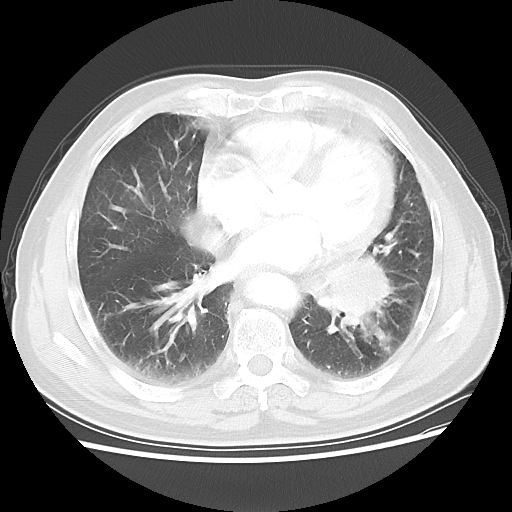
Chest CT, one axial slice; slice 25 of 56 in the series (ordered by position); reconstruction kernel LUNG; 120 kVp; lung window (W 1500 / L -600 HU); 5 mm slice thickness; 512 × 512 image matrix. Patient: male, 75 years. Case-level facts recorded for this patient, not image findings: clinical TNM (as recorded): T3 N0 M0.
Annotated regions visible in this slice (bounding box drawn by a radiologist):
- lung tumour (recorded histology: squamous cell carcinoma): bounding box [x1, y1, x2, y2] px = [317, 239, 418, 348]